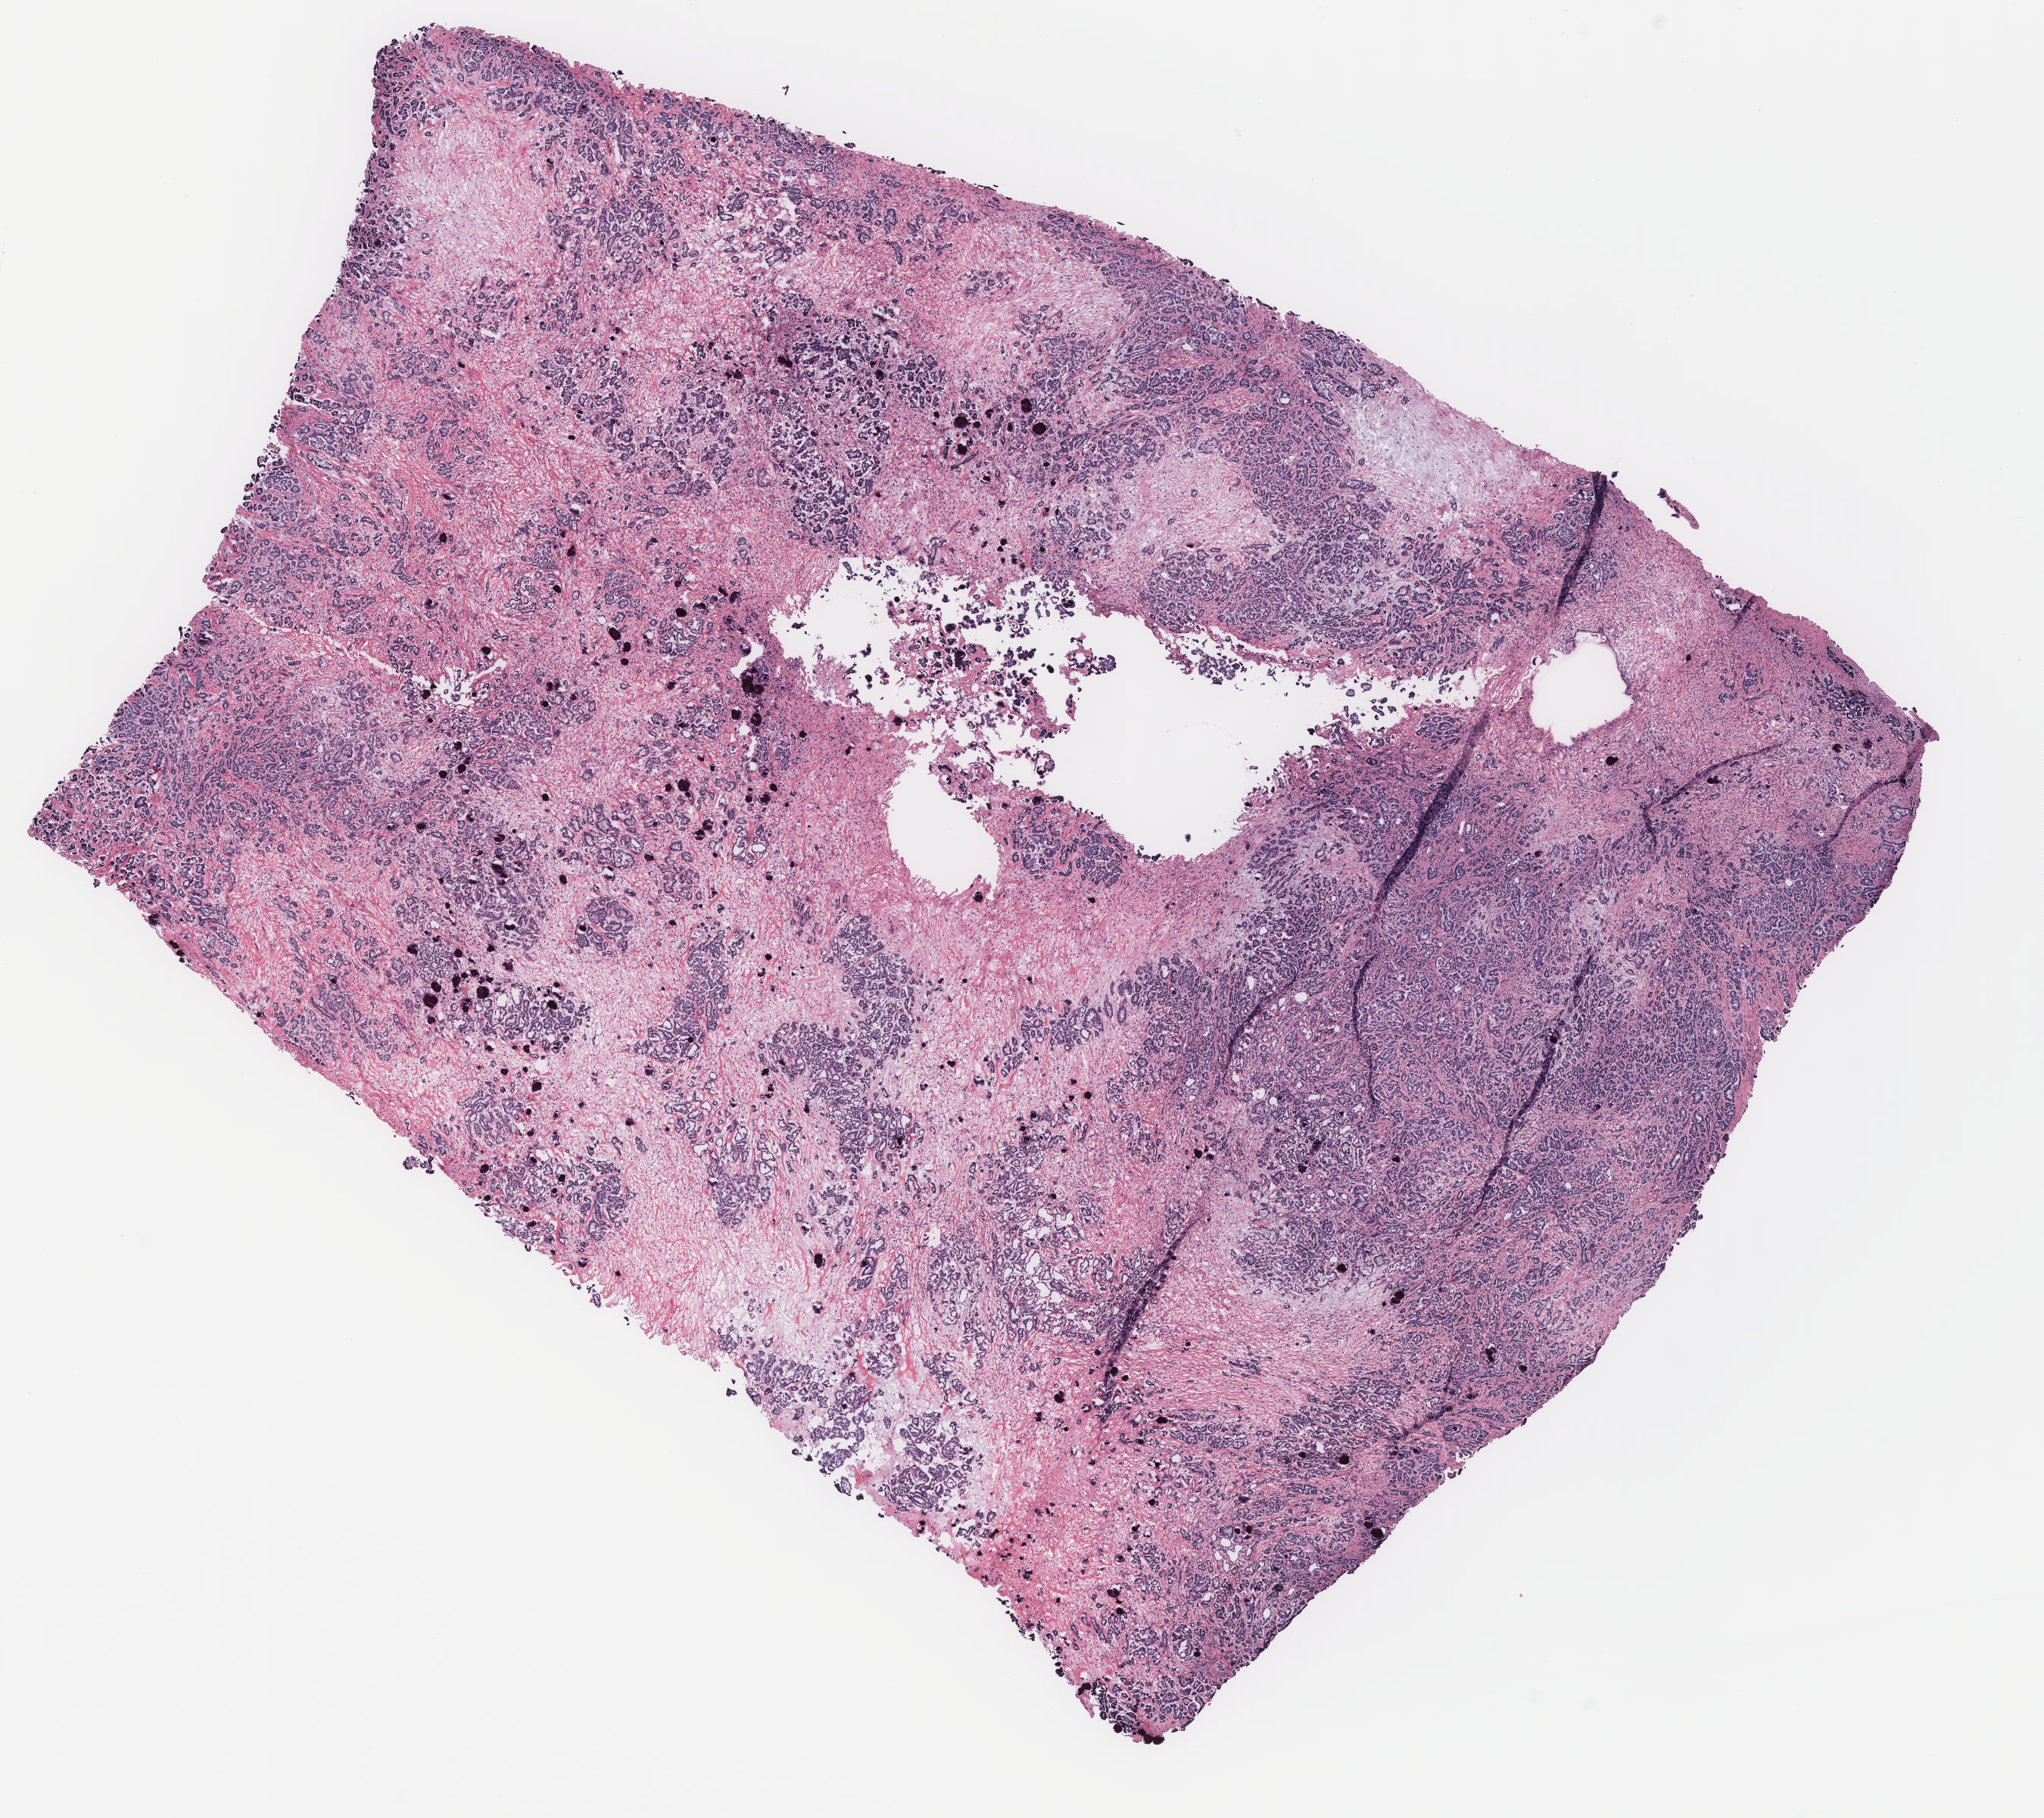
Digitized H&E-stained tissue section (whole slide) — shown as a low-resolution overview of the whole scanned area (about 10.8 x 9.6 mm); ovary, tumour tissue. 57-year-old female patient.
* primary tumour site (as recorded): ovary
* diagnosis: Serous adenocarcinoma, NOS